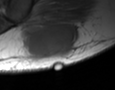
MRI of an extremity soft-tissue mass, one axial slice; position 16 of 35 along the scan axis; MR volume resampled by the dataset authors to the PET/CT grid (not the native acquisition matrix); 115 × 90 image matrix, field of view 112 × 88 mm. Male patient. Case-level facts recorded for this patient, not image findings: histological type: pleiomorphic leiomyosarcoma; grade: high; site of the primary tumour: left buttock.
Outlined on this slice (expert contour drawn on MRI and transferred to this co-registered scan by the dataset authors):
- gross tumour volume including surrounding oedema: box from (x=23, y=21) to (x=81, y=58) px
- gross tumour volume (mass): (x=24, y=23)–(x=79, y=58)